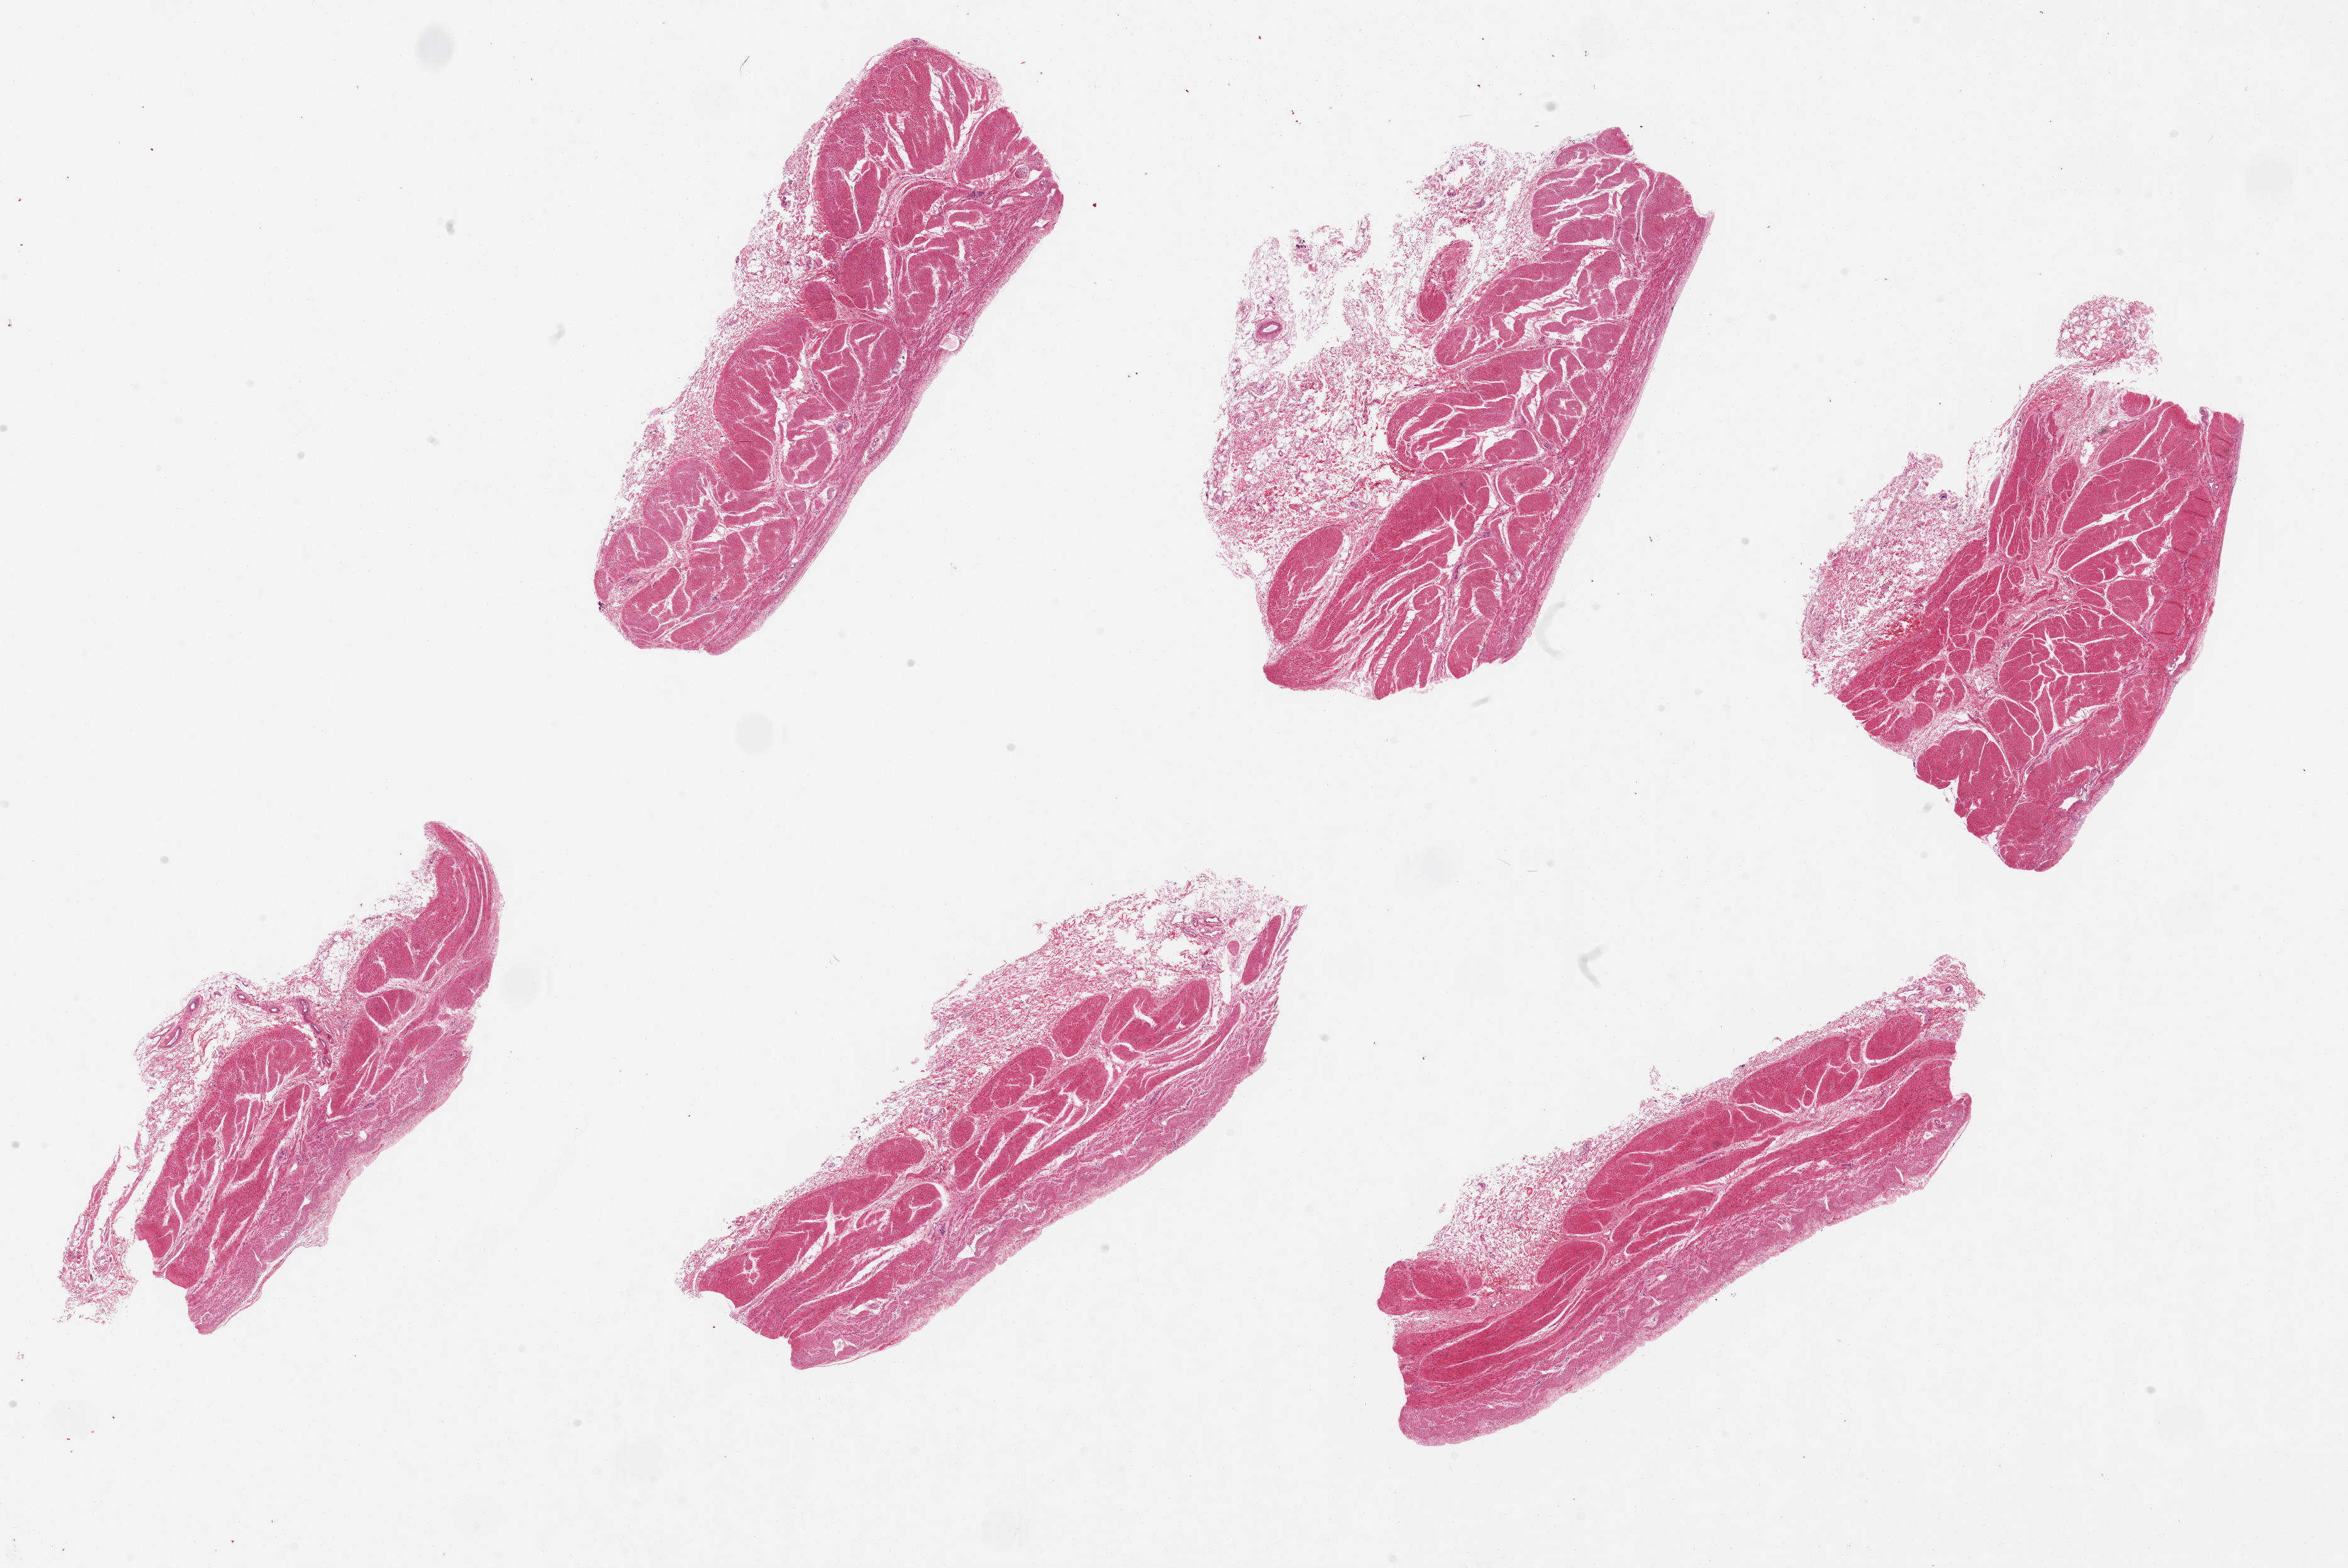
Digitized H&E-stained section — a low-resolution overview of the entire scanned area, about 29.5 x 19.7 mm (acquisition: 20x scan); PAXgene-fixed paraffin-embedded (PFPE) section; sampled site (target tissue): stomach; tissue donor sample. Male donor.
- pathologist's review note for this sample: 6 pieces up to 8x4.5 mm; all have had their mucosa removed so that only the muscularis and submucosa remain